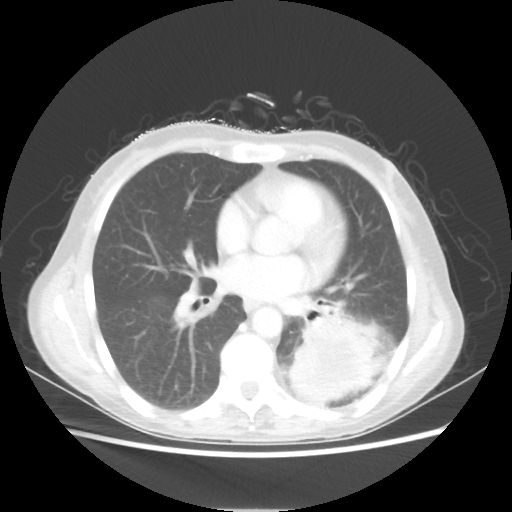
Chest CT, one axial slice. Position 27 of 56 along the scan axis. Reconstruction kernel STANDARD. Lung window (W 1500 / L -600 HU). 5 mm slice thickness. 512 × 512 image matrix, field of view 360 × 360 mm. Patient: female, 53 years. Case-level facts recorded for this patient, not image findings: clinical TNM (as recorded): T3 N0 M0.
Structures marked on this image (bounding box drawn by a radiologist):
- lung tumour (recorded histology: adenocarcinoma): bounding box <290,308,385,404> (left, top, right, bottom; pixels)